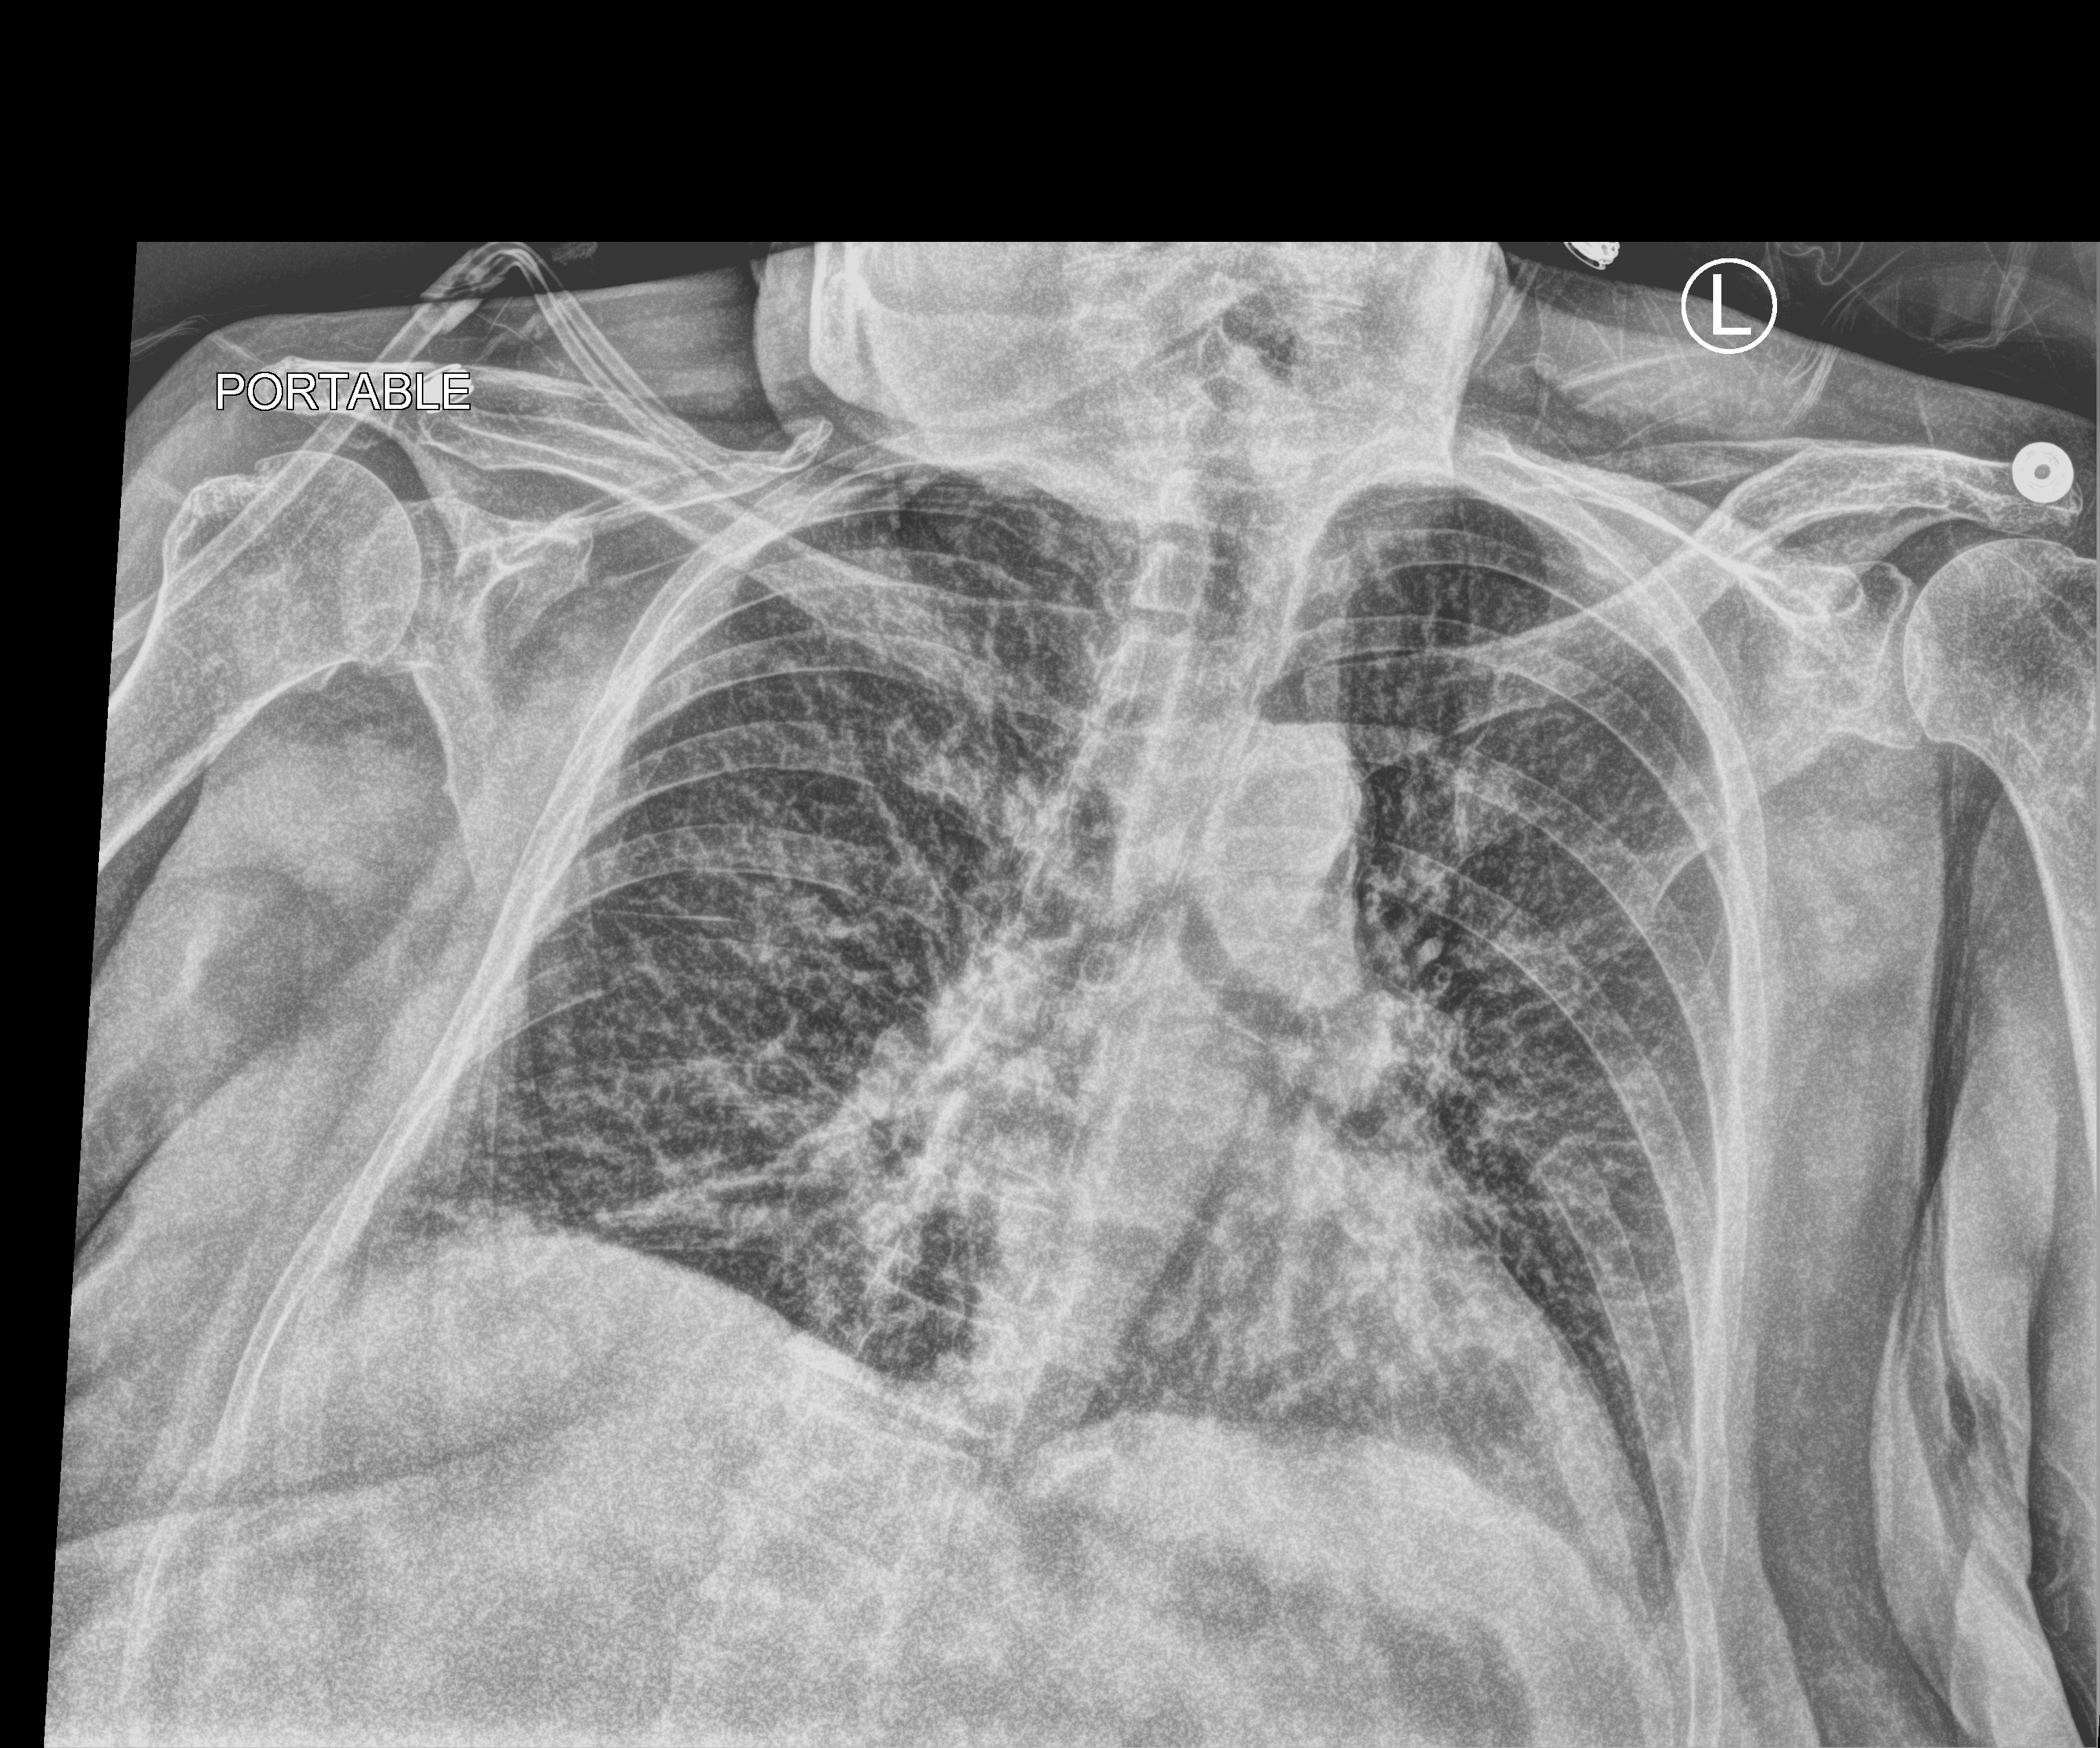
Portable chest radiograph, anteroposterior (AP) projection. Female patient hospitalised with COVID-19, age 75–90 years.
Admission-level facts for this patient (not findings on this image; timing relative to this image not recorded): admitted to intensive care during this hospital stay: no; chronic kidney disease (admission record): yes.